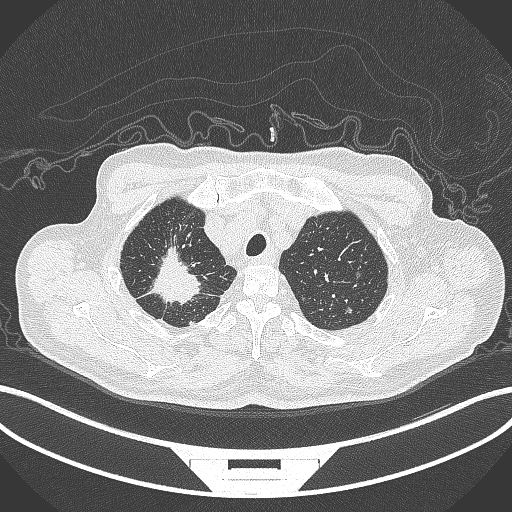
Chest CT, one axial slice. Position 328 of 407 along the scan axis. Reconstruction kernel B70f. 120 kVp. Lung window (W 1500 / L -600 HU). 512 × 512 image matrix, field of view 400 × 400 mm. Male patient, age 69 years. Case-level facts recorded for this patient, not image findings: clinical TNM (as recorded): T1c N1 M1.
Annotated regions visible in this slice (bounding box drawn by a radiologist):
- lung tumour (recorded histology: adenocarcinoma): bounding box [x1, y1, x2, y2] px = [137, 242, 207, 307]